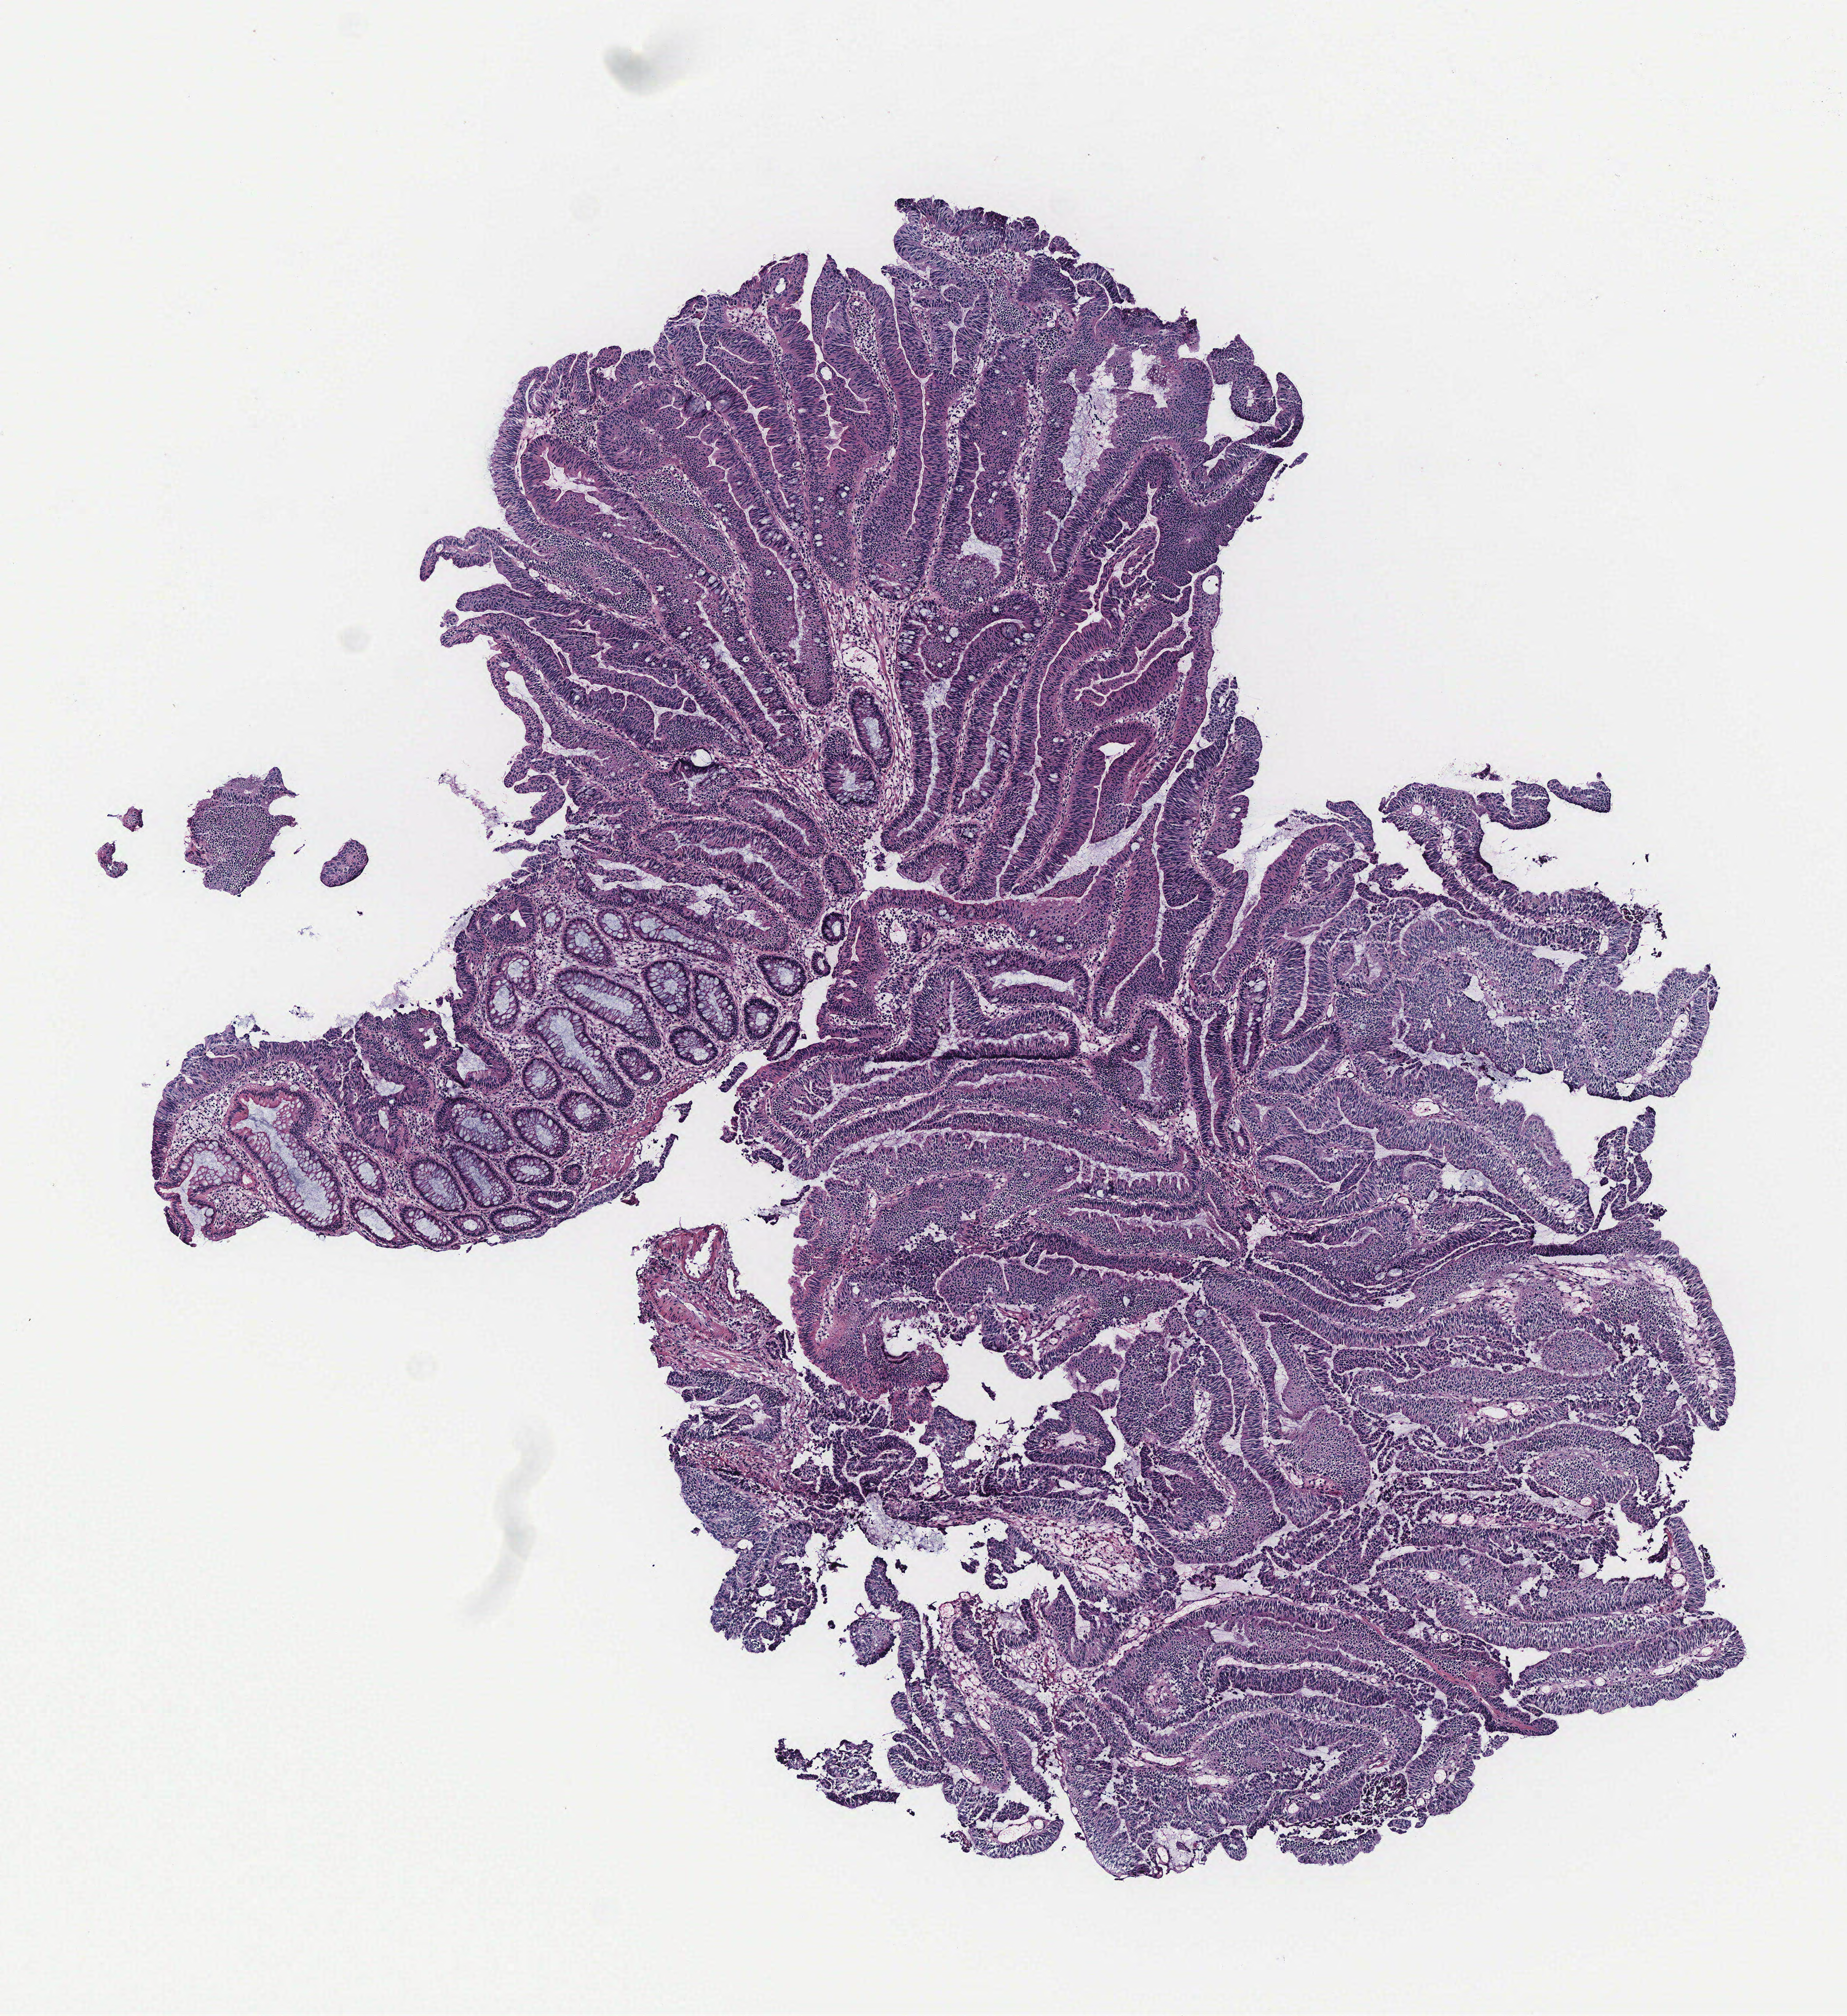
Whole-slide histology image, H&E-stained, low-resolution overview of the scanned area, about 5.5 x 6.0 mm (slide scanned at 40x). Colon, tissue type not recorded.
Patient diagnosis (cohort enrolment): colon cancer (colon).